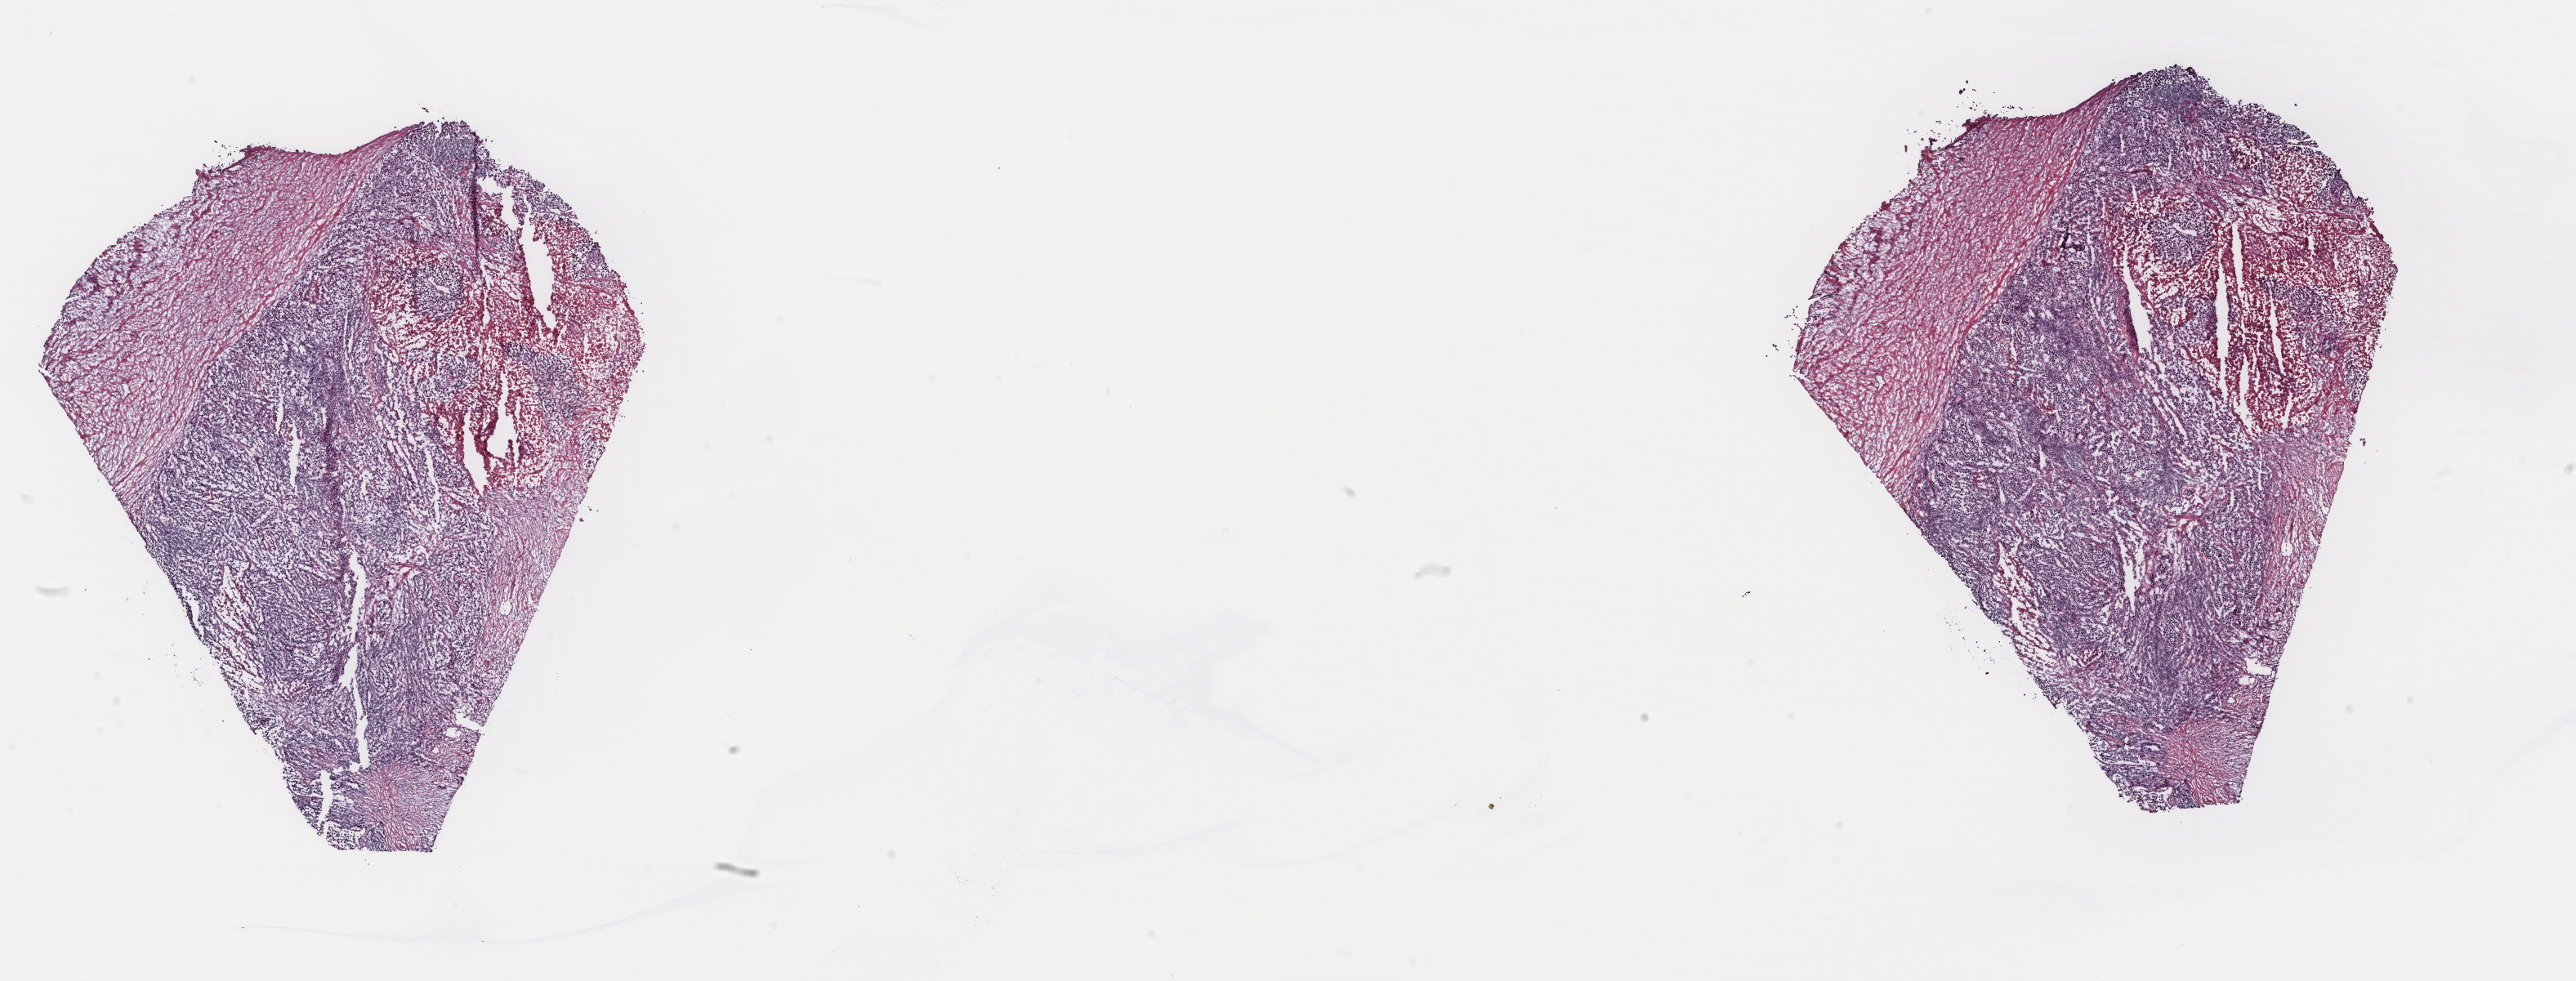
Digitized H&E-stained tissue section (whole slide), shown as a low-resolution overview of the whole scanned area (about 25.0 x 9.5 mm, from a 40x scan). Frozen section from the top of the tissue portion. Metastatic tumour sample. Female, age 23 years at initial diagnosis. Slide review estimates, as recorded: tumour cells 60%, tumour nuclei 80%, normal cells 0%, stromal cells 25%, necrosis 15%. Inflammatory infiltration, as recorded: lymphocyte infiltration 0%, monocyte infiltration 0%, neutrophil infiltration 0%.
This section: metastatic tumour tissue. Patient diagnosis: Malignant melanoma, NOS.